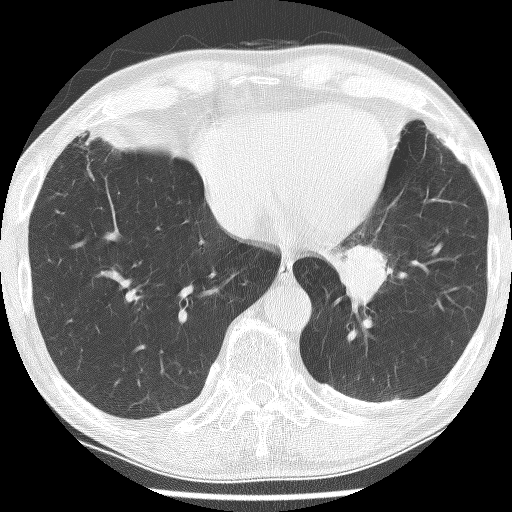
Chest CT (low-dose screening protocol), one axial image; first (baseline) screen; lung window (W 1500 / L -600 HU); lung (sharp) reconstruction kernel (BONE); slice 176 of 226 in the series; 512 × 512 image matrix. Male, age 74 years at enrolment. Current smoker at enrolment.
- Expert reader's lesion annotation, bounding box [x1, y1, x2, y2] px = [315, 223, 419, 316].
- The exam's reader record, not a measurement of the box and not confirmed to be the same lesion: non-calcified nodule or mass ≥4 mm, left lower lobe, 30 × 27 mm, spiculated (stellate) margins, soft tissue attenuation.
- Later outcome: lung cancer diagnosed 151 days after this screen — adenocarcinoma, NOS, left lower lobe, stage IIIA (AJCC 6th edition), 49 mm at pathology.